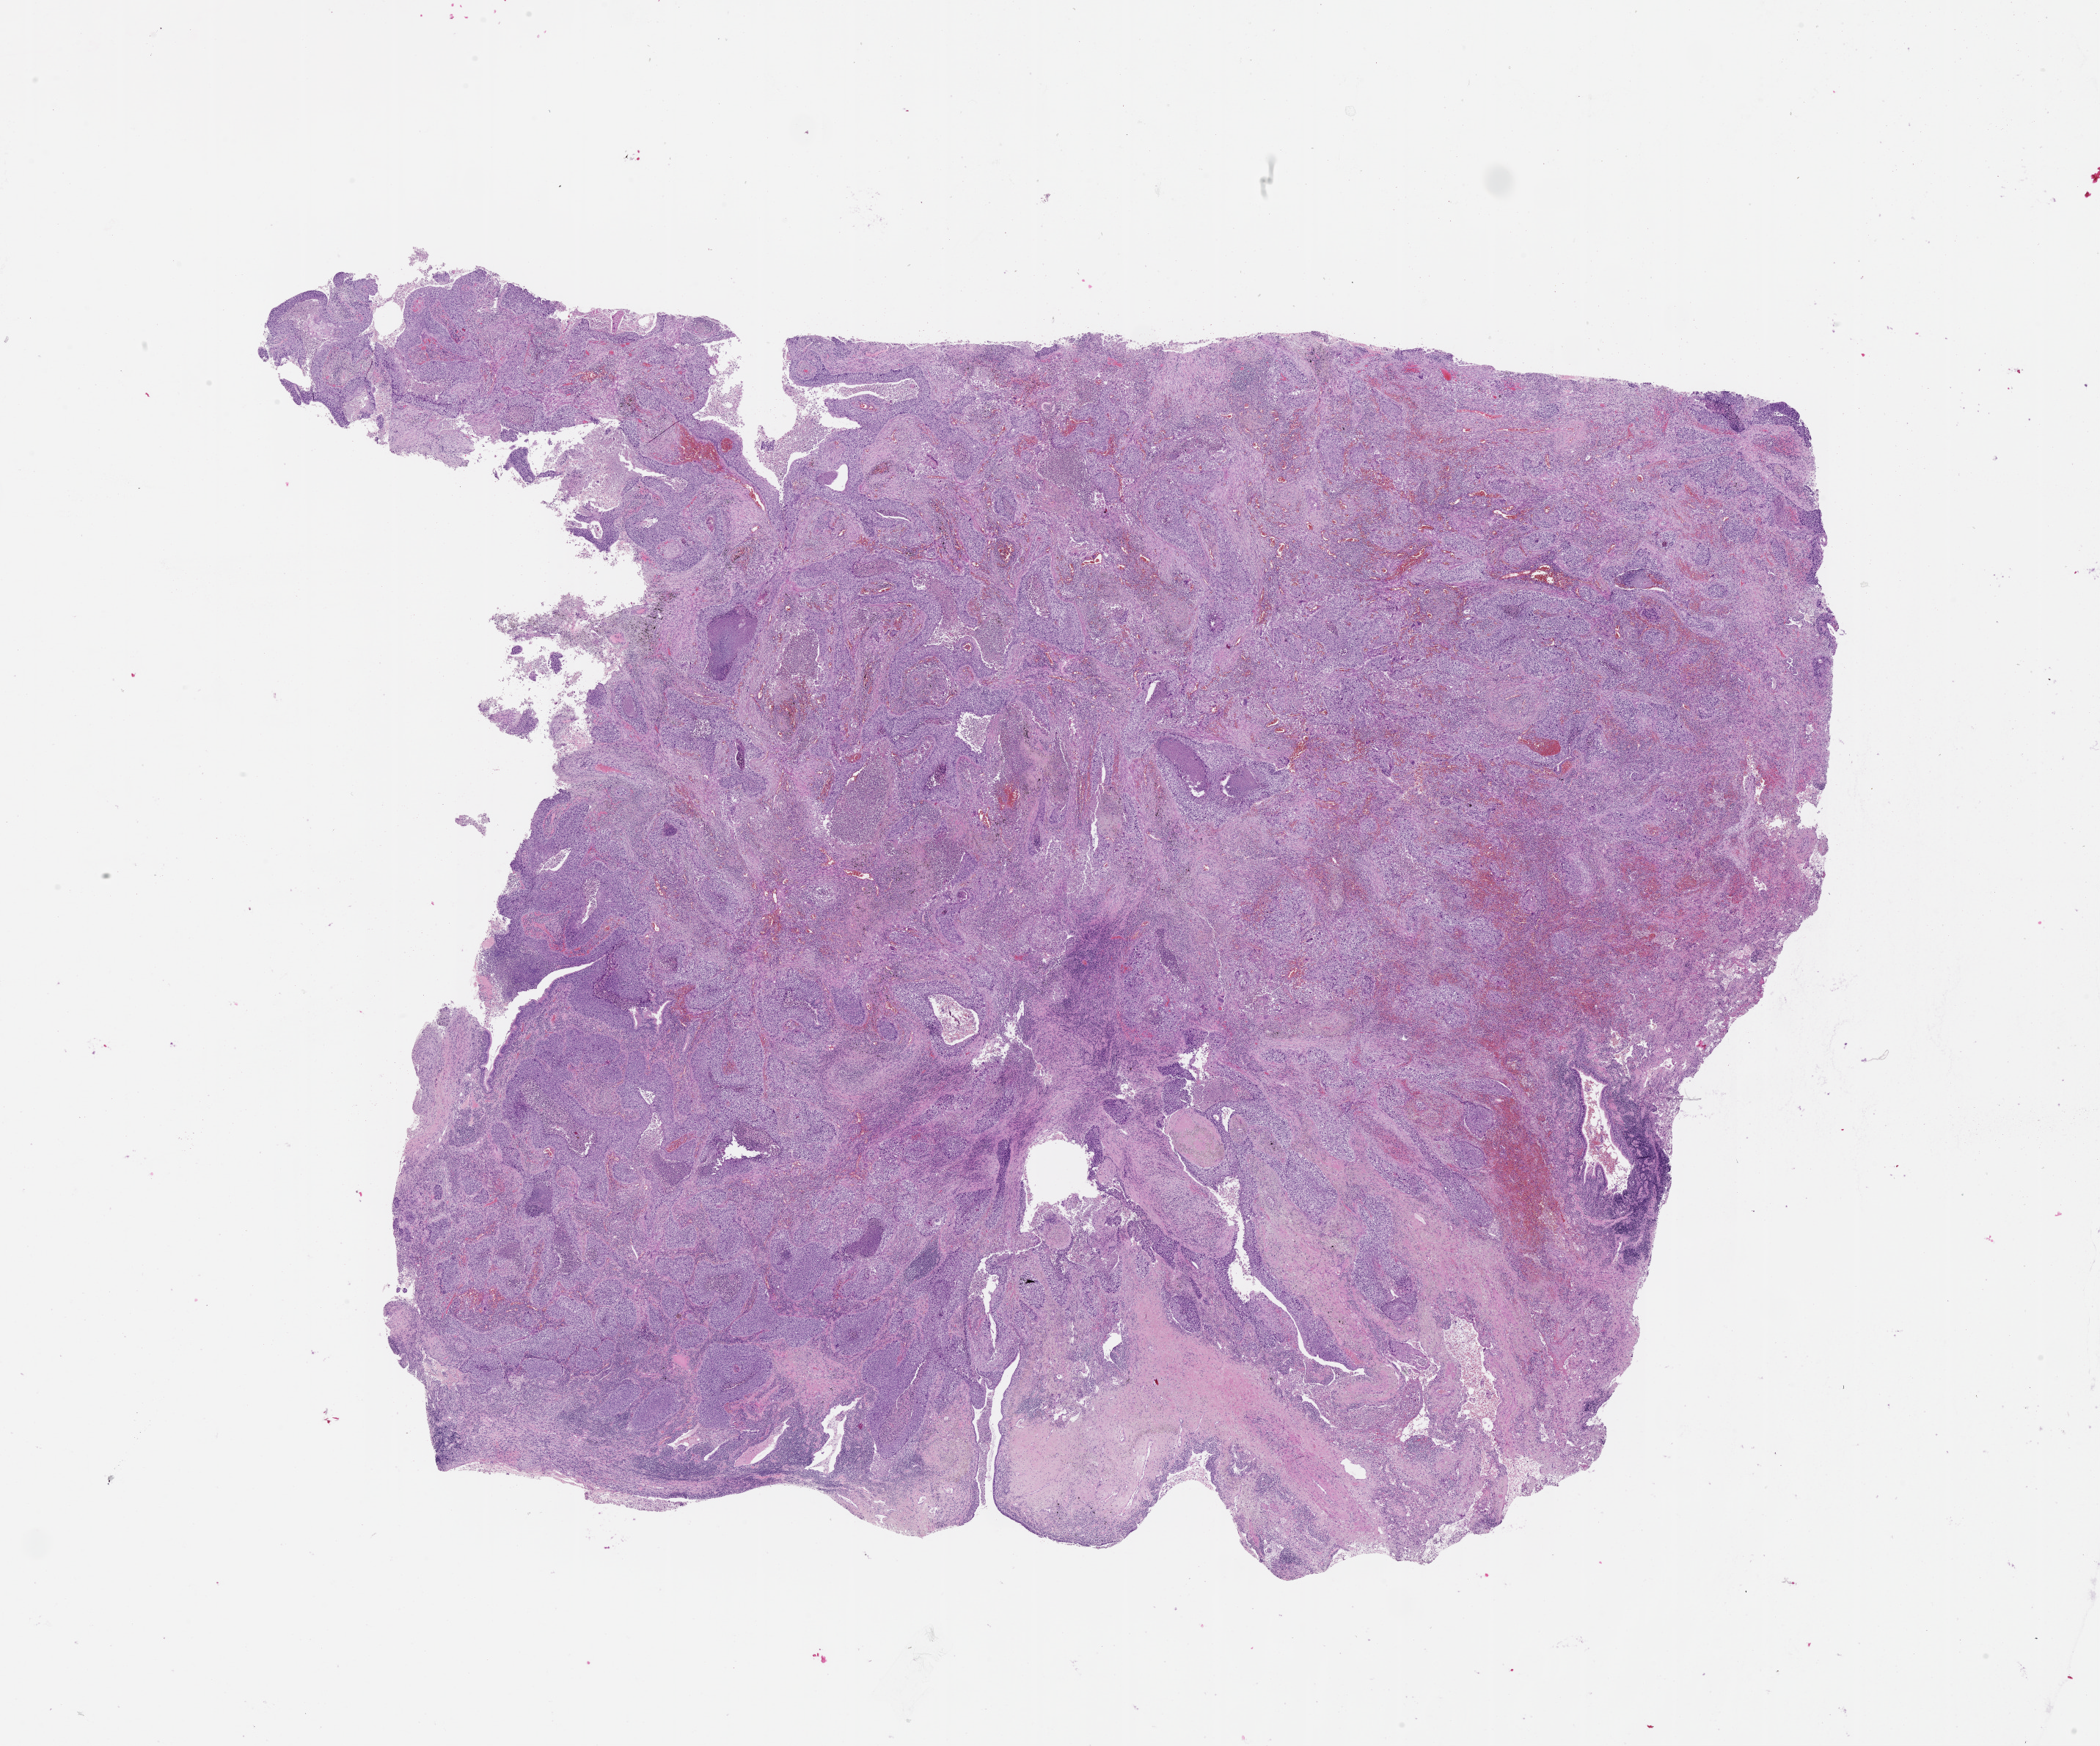
Whole-slide histology image, H&E-stained, whole scanned area (about 23.1 x 19.2 mm) shown as a low-resolution overview. Tumour tissue sample, lung. Patient: male, age 77 years.
Patient diagnosis (cohort enrolment): squamous cell carcinoma (lung).